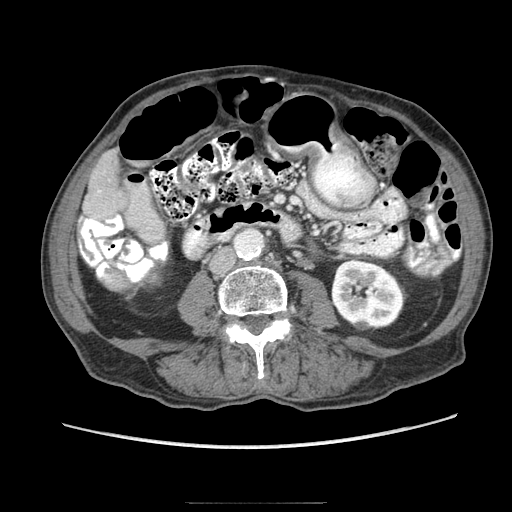
Contrast-enhanced abdominal CT (liver protocol), one axial slice. Position 13 of 83 along the scan axis. Reconstruction kernel STANDARD. Soft-tissue window (W 400 / L 40 HU). 512 × 512 image matrix, field of view 360 × 360 mm. Case-level facts recorded for this patient, not image findings: diagnosis: hepatocellular carcinoma (patient treated with transarterial chemoembolisation; whether this scan precedes or follows treatment is not stated here); TNM stage (as recorded): Stage-I; Child-Pugh class: A; tumour differentiation: moderately differentiated; tumour nodularity: uninodular.
Structures marked on this image (semi-automatically segmented with operator editing):
- liver parenchyma outside the tumour (the mass and vessels are separate outlines, so this box may not span the whole liver): bounding box [x1, y1, x2, y2] px = [82, 150, 128, 218]
- liver vessels: [98, 190, 101, 193]